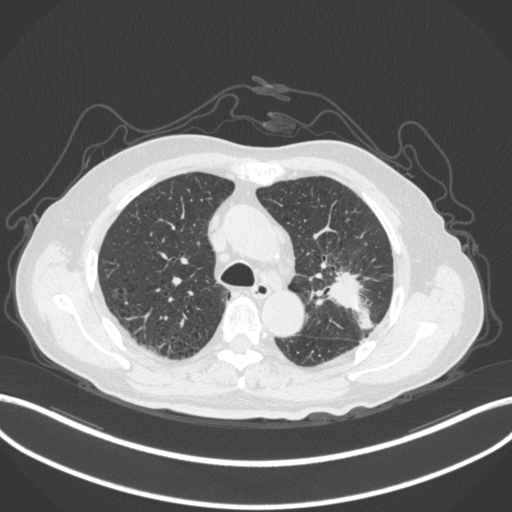
Chest CT, one axial slice; position 198 of 331 along the scan axis; reconstruction kernel B31f; lung window (W 1500 / L -600 HU); 1 mm slice thickness; 512 × 512 image matrix. Patient: male, 79 years. Case-level facts recorded for this patient, not image findings: clinical TNM (as recorded): T2a N1 M1; histopathological grade: G3.
Outlined on this slice (rectangle marked by the reading radiologist):
- lung tumour (recorded histology: adenocarcinoma): bounding box <325,264,376,337> (left, top, right, bottom; pixels)